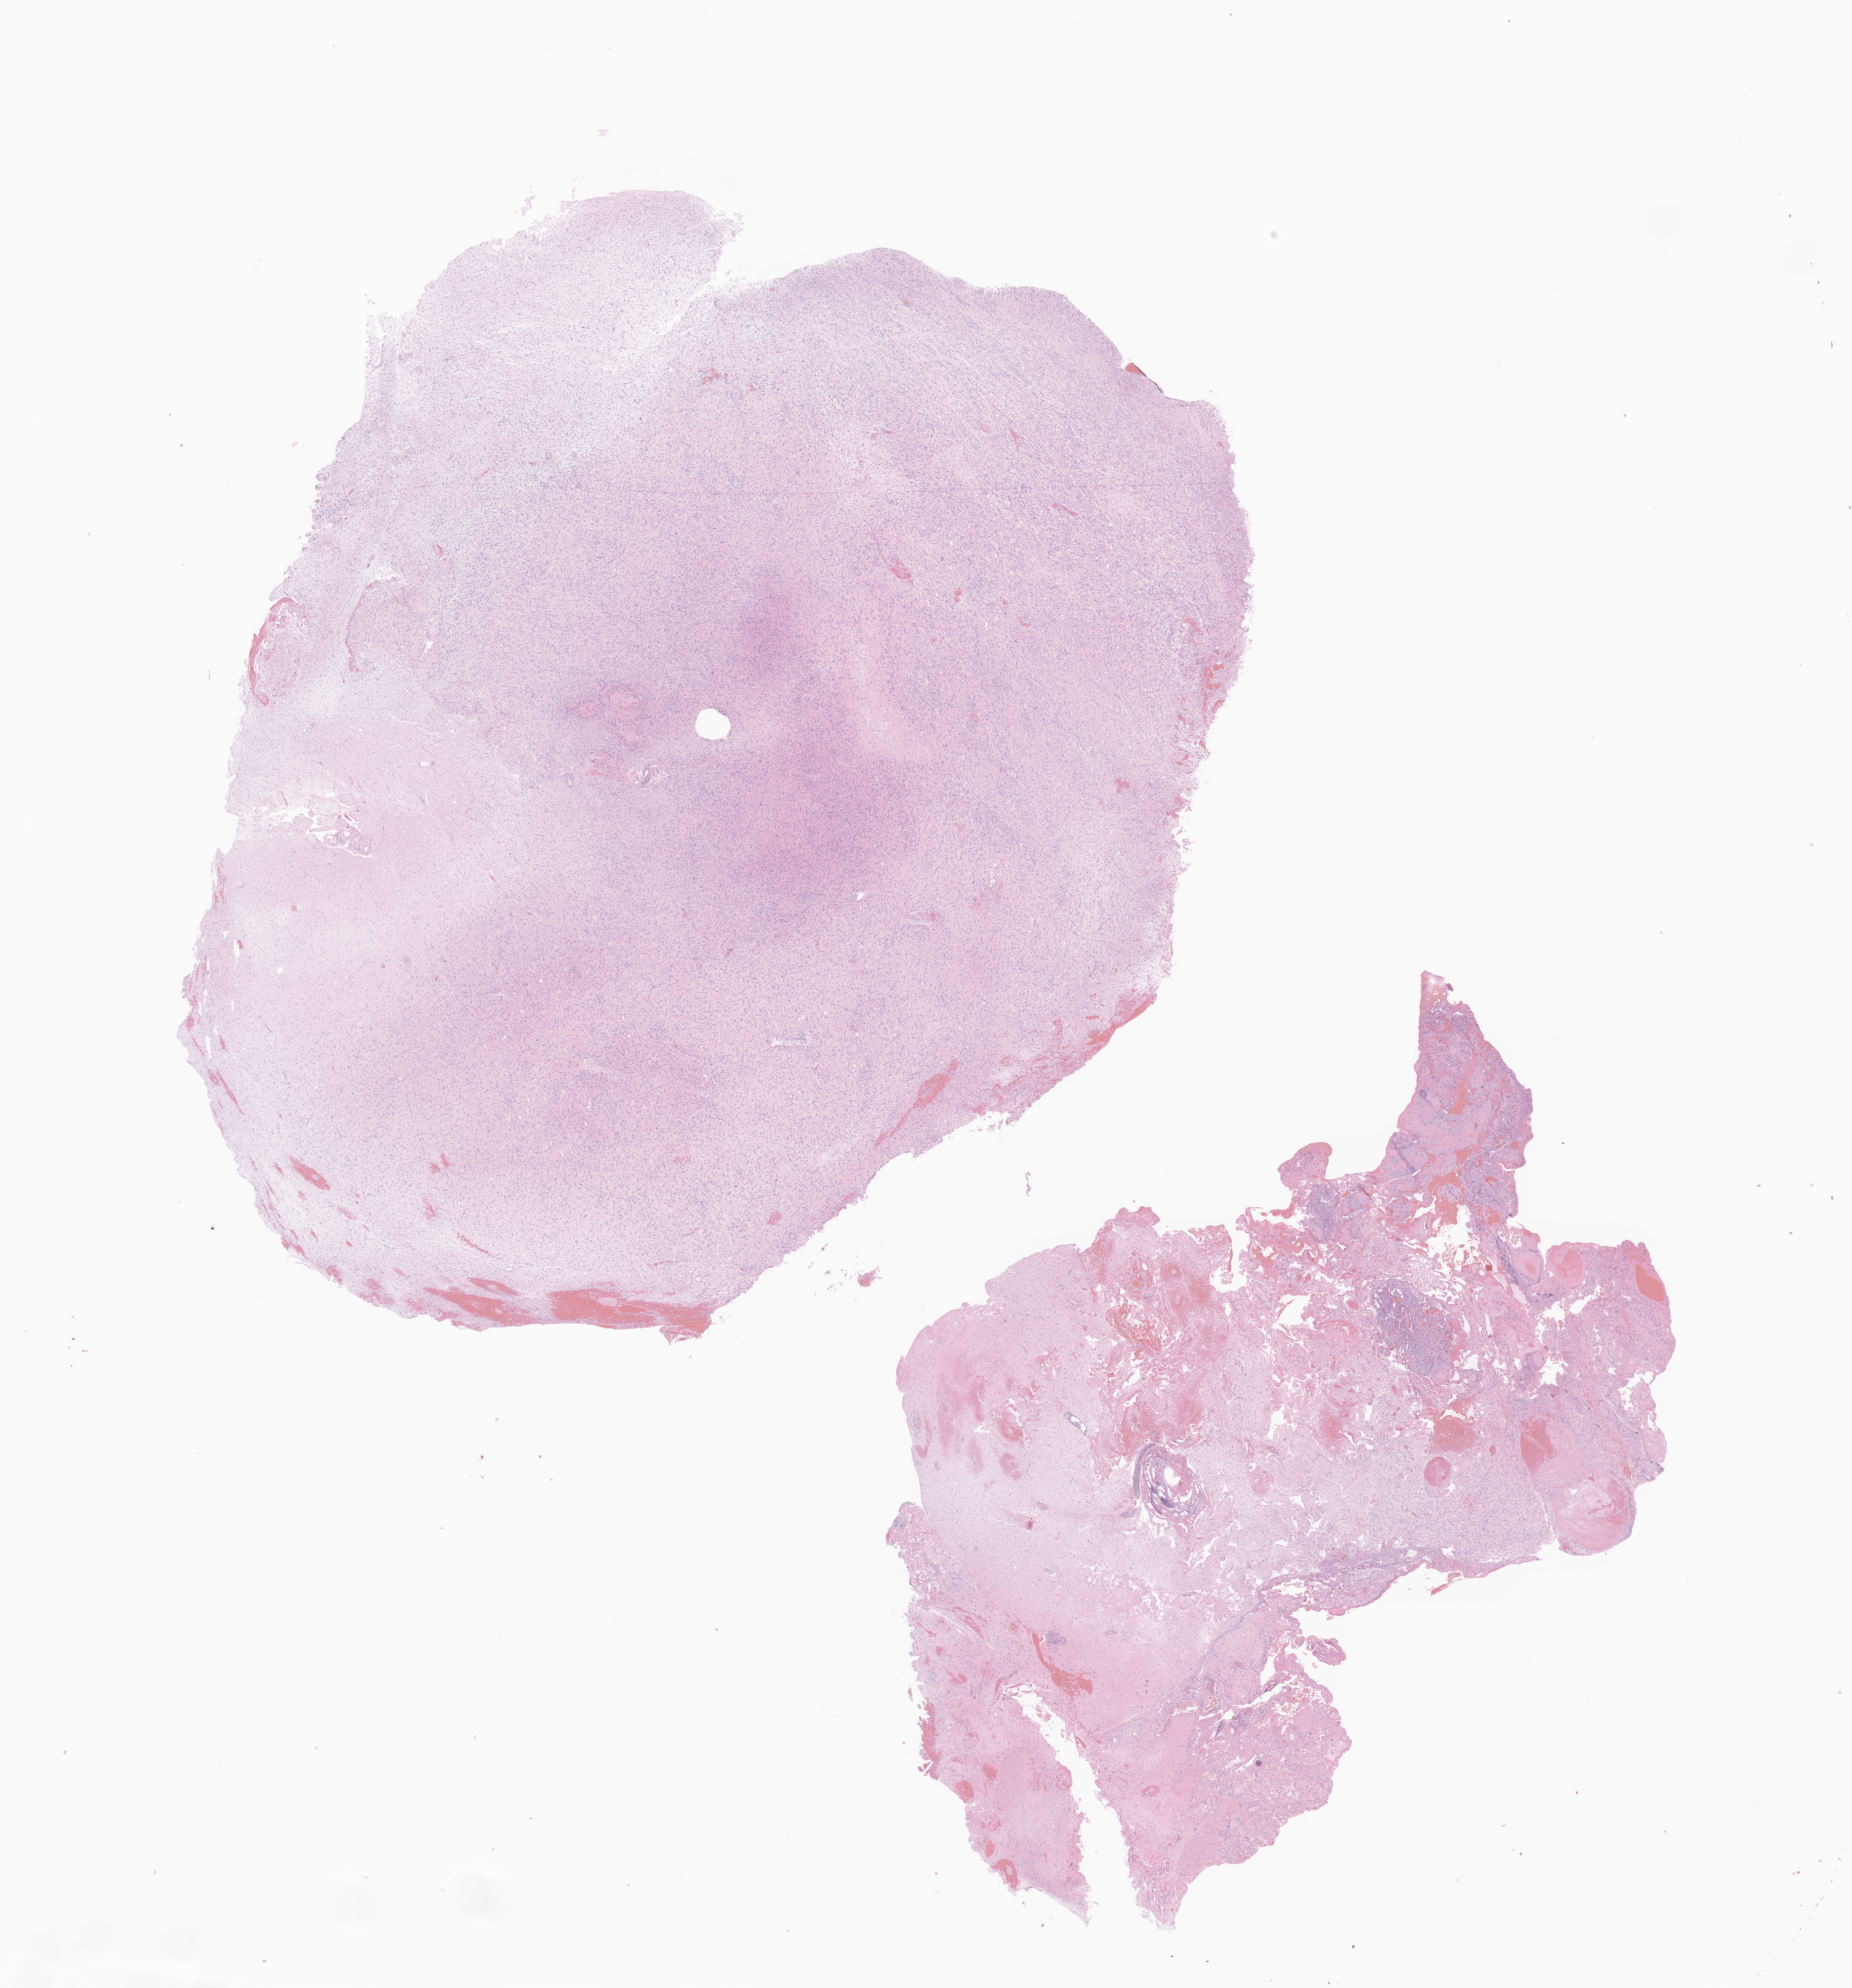
Digitized hematoxylin and eosin (H&E)-stained section of tumor tissue from the brain stem — a low-resolution overview of the entire scanned area, about 20.4 x 21.9 mm, formalin-fixed paraffin-embedded section. Male patient, age 223 months (18 years 7 months).
* recorded diagnosis: Glioma, malignant